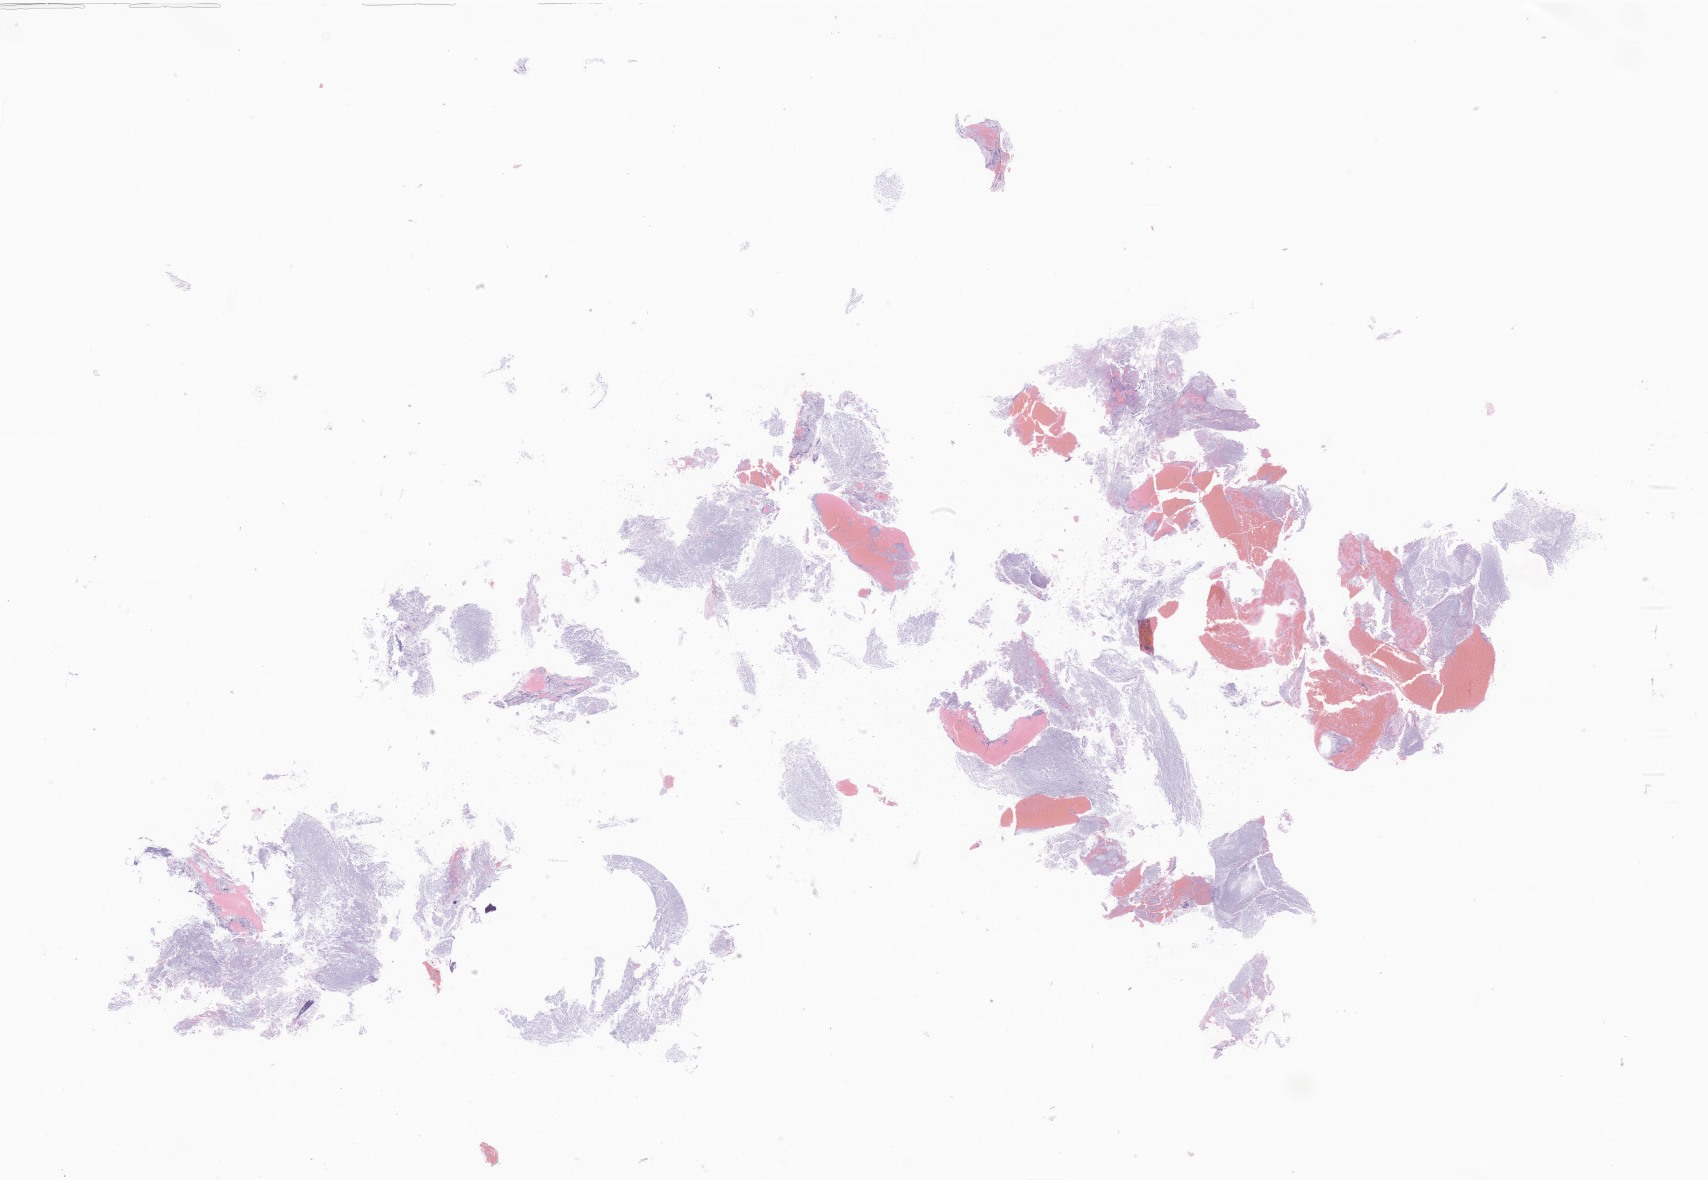
Hematoxylin and eosin (H&E) whole-slide image of tumor tissue from the head and neck, whole scanned area (about 28.8 x 19.9 mm) shown as a low-resolution overview; FFPE section. Male patient, age 234 days.
Tissue or organ of origin (case record): head, face or neck. Recorded diagnosis: Neoplasm, uncertain whether benign or malignant.